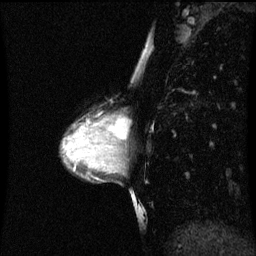
Breast MRI (dynamic contrast-enhanced), one sagittal slice; position 31 of 60 along the scan axis; dynamic contrast-enhanced series, image 2 of 3 at this slice position (ordered by acquisition); 1.5 T; TE 4.2 ms, TR 8.9 ms; 256 × 256 image matrix. Female patient, age 33 years. From the clinical record (not read from this slice): setting: breast cancer imaged before/during neoadjuvant chemotherapy; receptor status: HER2-positive.
Annotated regions visible in this slice (semi-automatic segmentation, software-assisted and operator-edited):
- analysis volume of interest (the breast-tissue region the enhancement analysis was run in; not a lesion): box from (x=107, y=108) to (x=123, y=147) px
- tumour enhancement mask (voxels above the 70 % enhancement threshold inside the analysis volume of interest): (x=110, y=118)–(x=123, y=141)